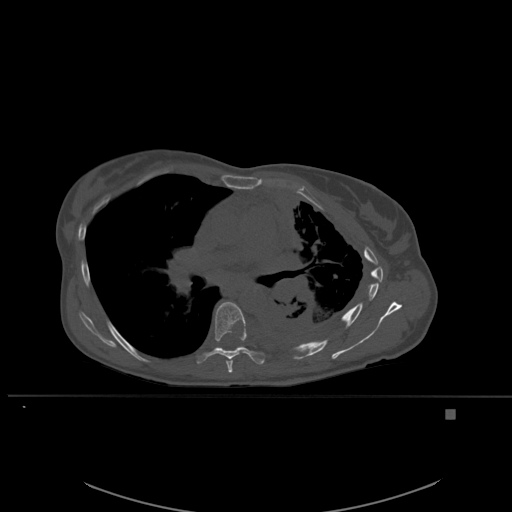
CT including the spine, one axial slice; slice 368 of 537 in the series (ordered by position); bone window (W 1800 / L 400 HU); 512 × 512 image matrix, field of view 440 × 440 mm. Female patient, age 45 years. Case-level facts recorded for this patient, not image findings: primary cancer: lung.
Outlined on this slice (semi-automatically segmented with operator editing):
- T6 vertebra: bounding box <226,360,233,373> (left, top, right, bottom; pixels)
- T7 vertebra: <197,301,264,365>